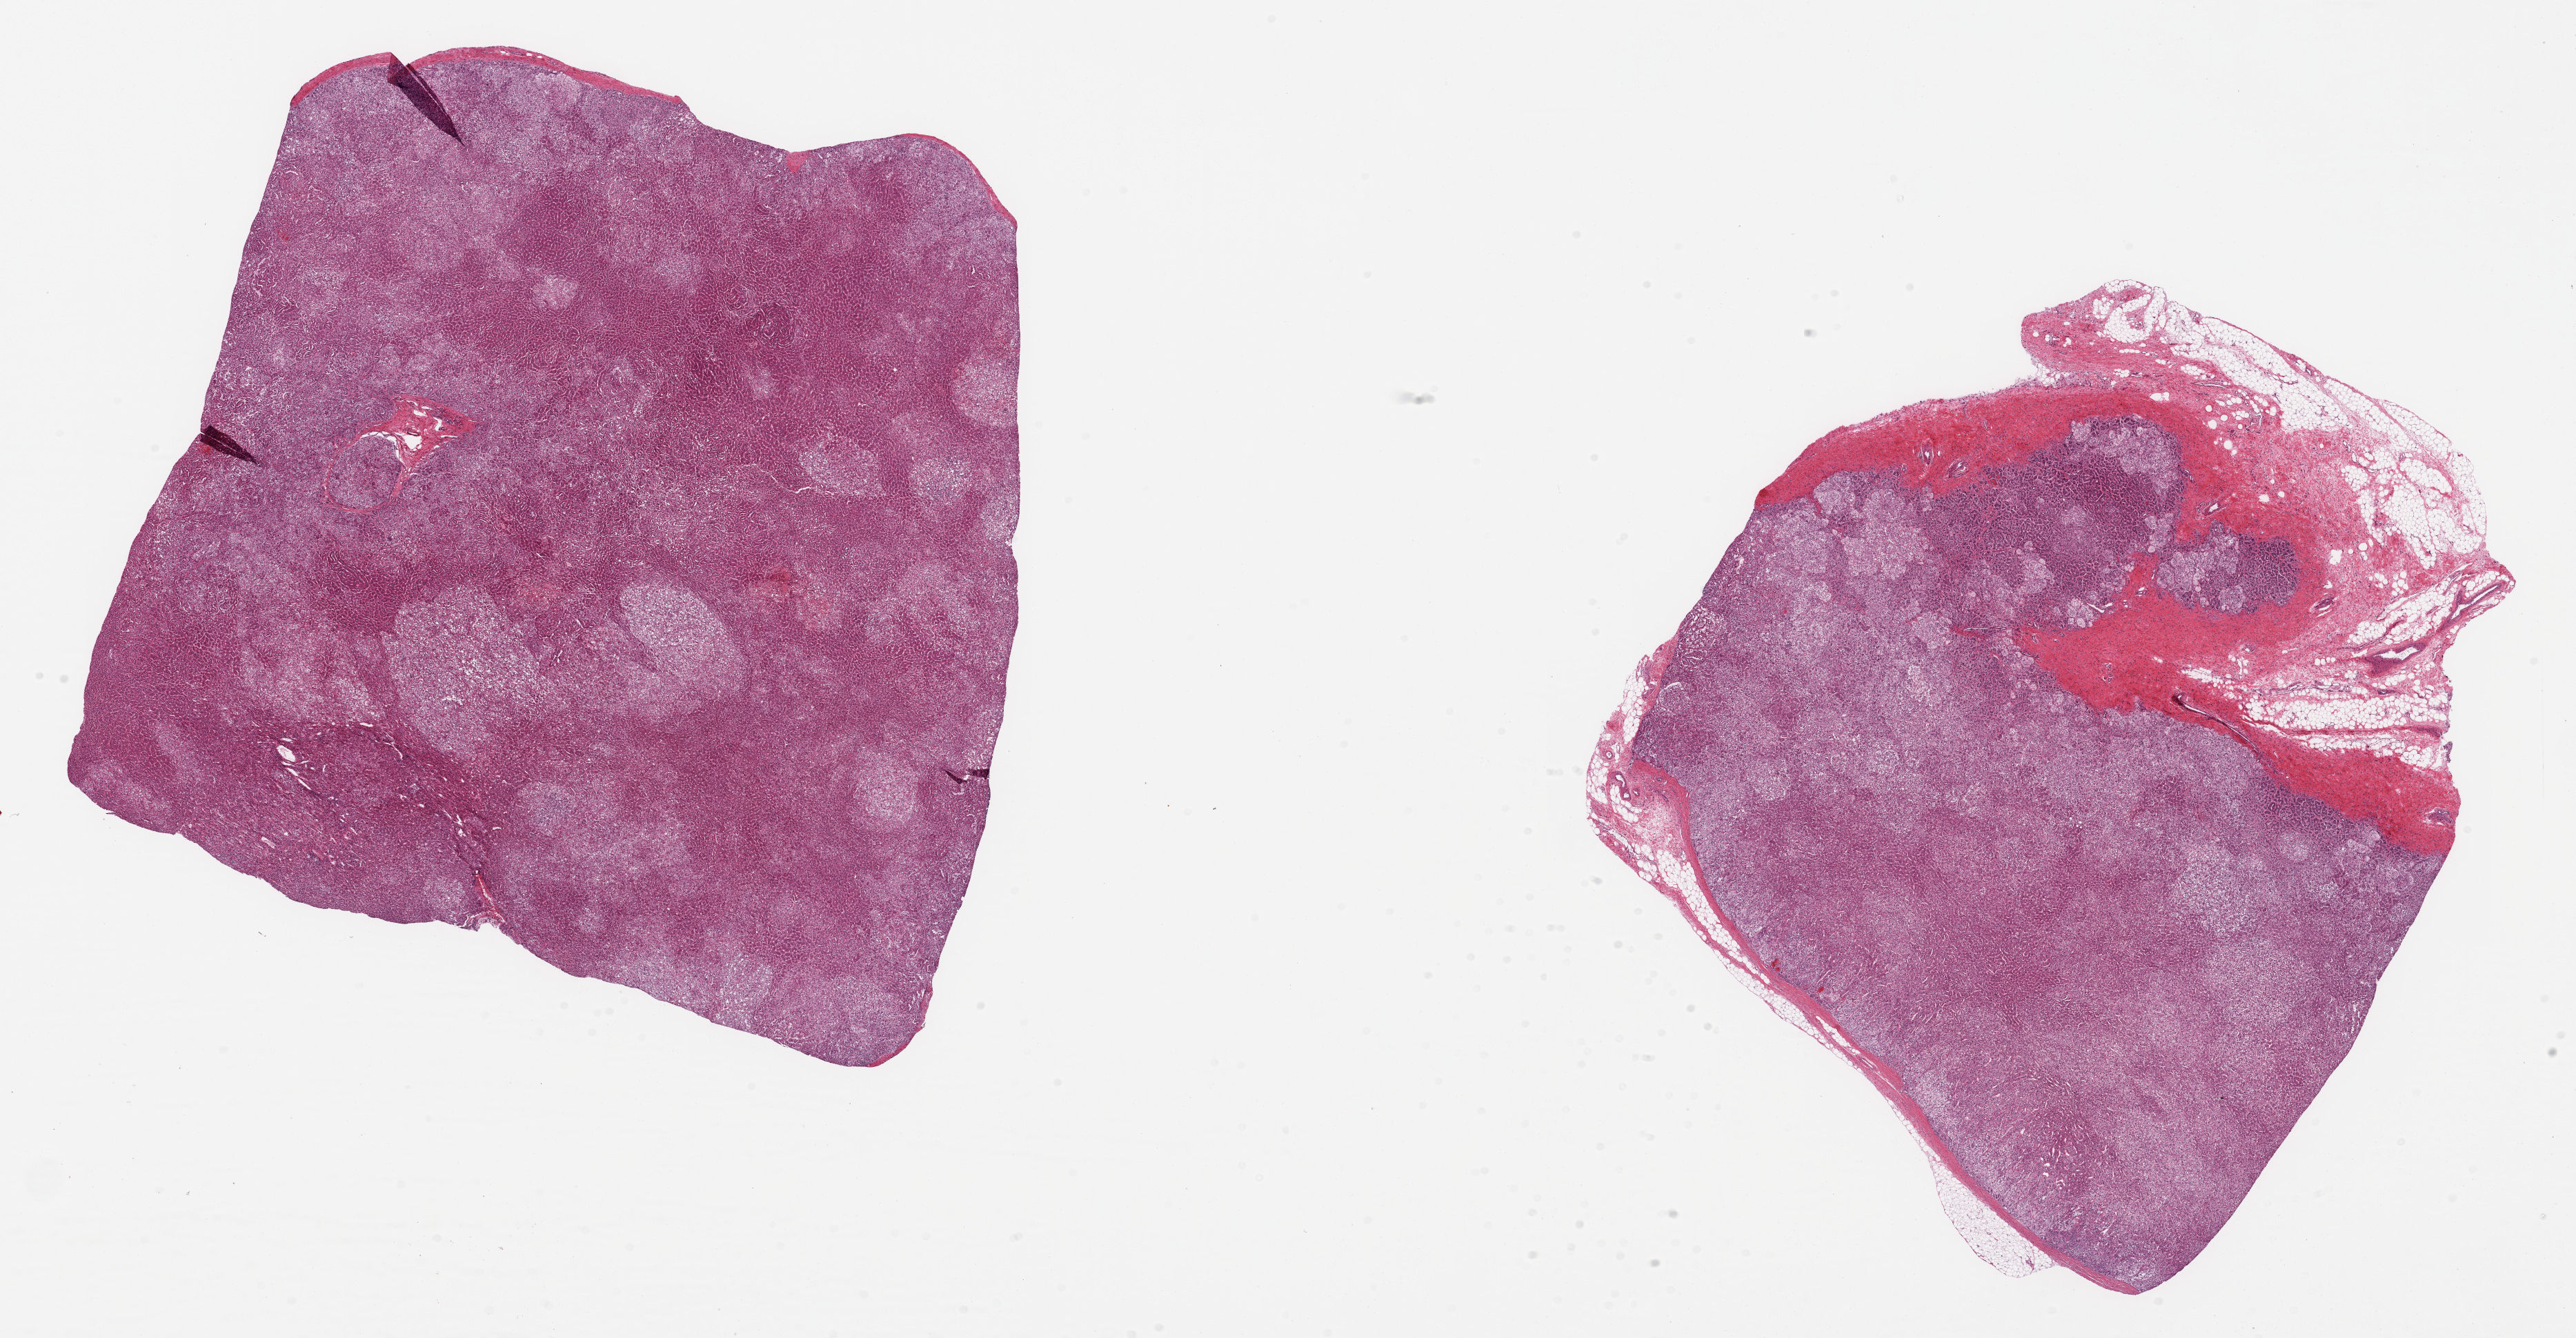
Digitized H&E-stained section — a low-resolution overview of the entire scanned area, about 29.5 x 15.3 mm, PAXgene-fixed, paraffin-embedded tissue, sampled site (target tissue): adrenal gland, tissue donor sample. Female donor.
Pathologist's review note for this sample: 2 pieces; adrenal cortex; one with ~20% attached fibroadipose tissue.